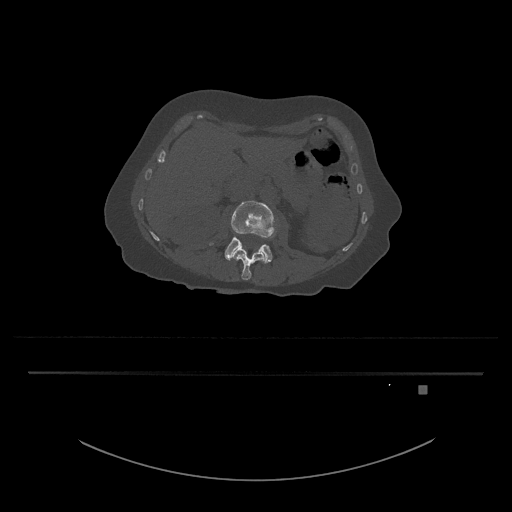
CT including the spine, one axial slice; slice 458 of 797 in the series (ordered by position); bone window (W 1800 / L 400 HU); 0.5 mm slice thickness; 512 × 512 image matrix, field of view 500 × 500 mm. Female patient, age 57 years. Case-level facts recorded for this patient, not image findings: primary cancer: cervical.
Structures marked on this image (semi-automatic segmentation, software-assisted and operator-edited):
- L3 vertebra: bounding box <209,201,277,263> (left, top, right, bottom; pixels)